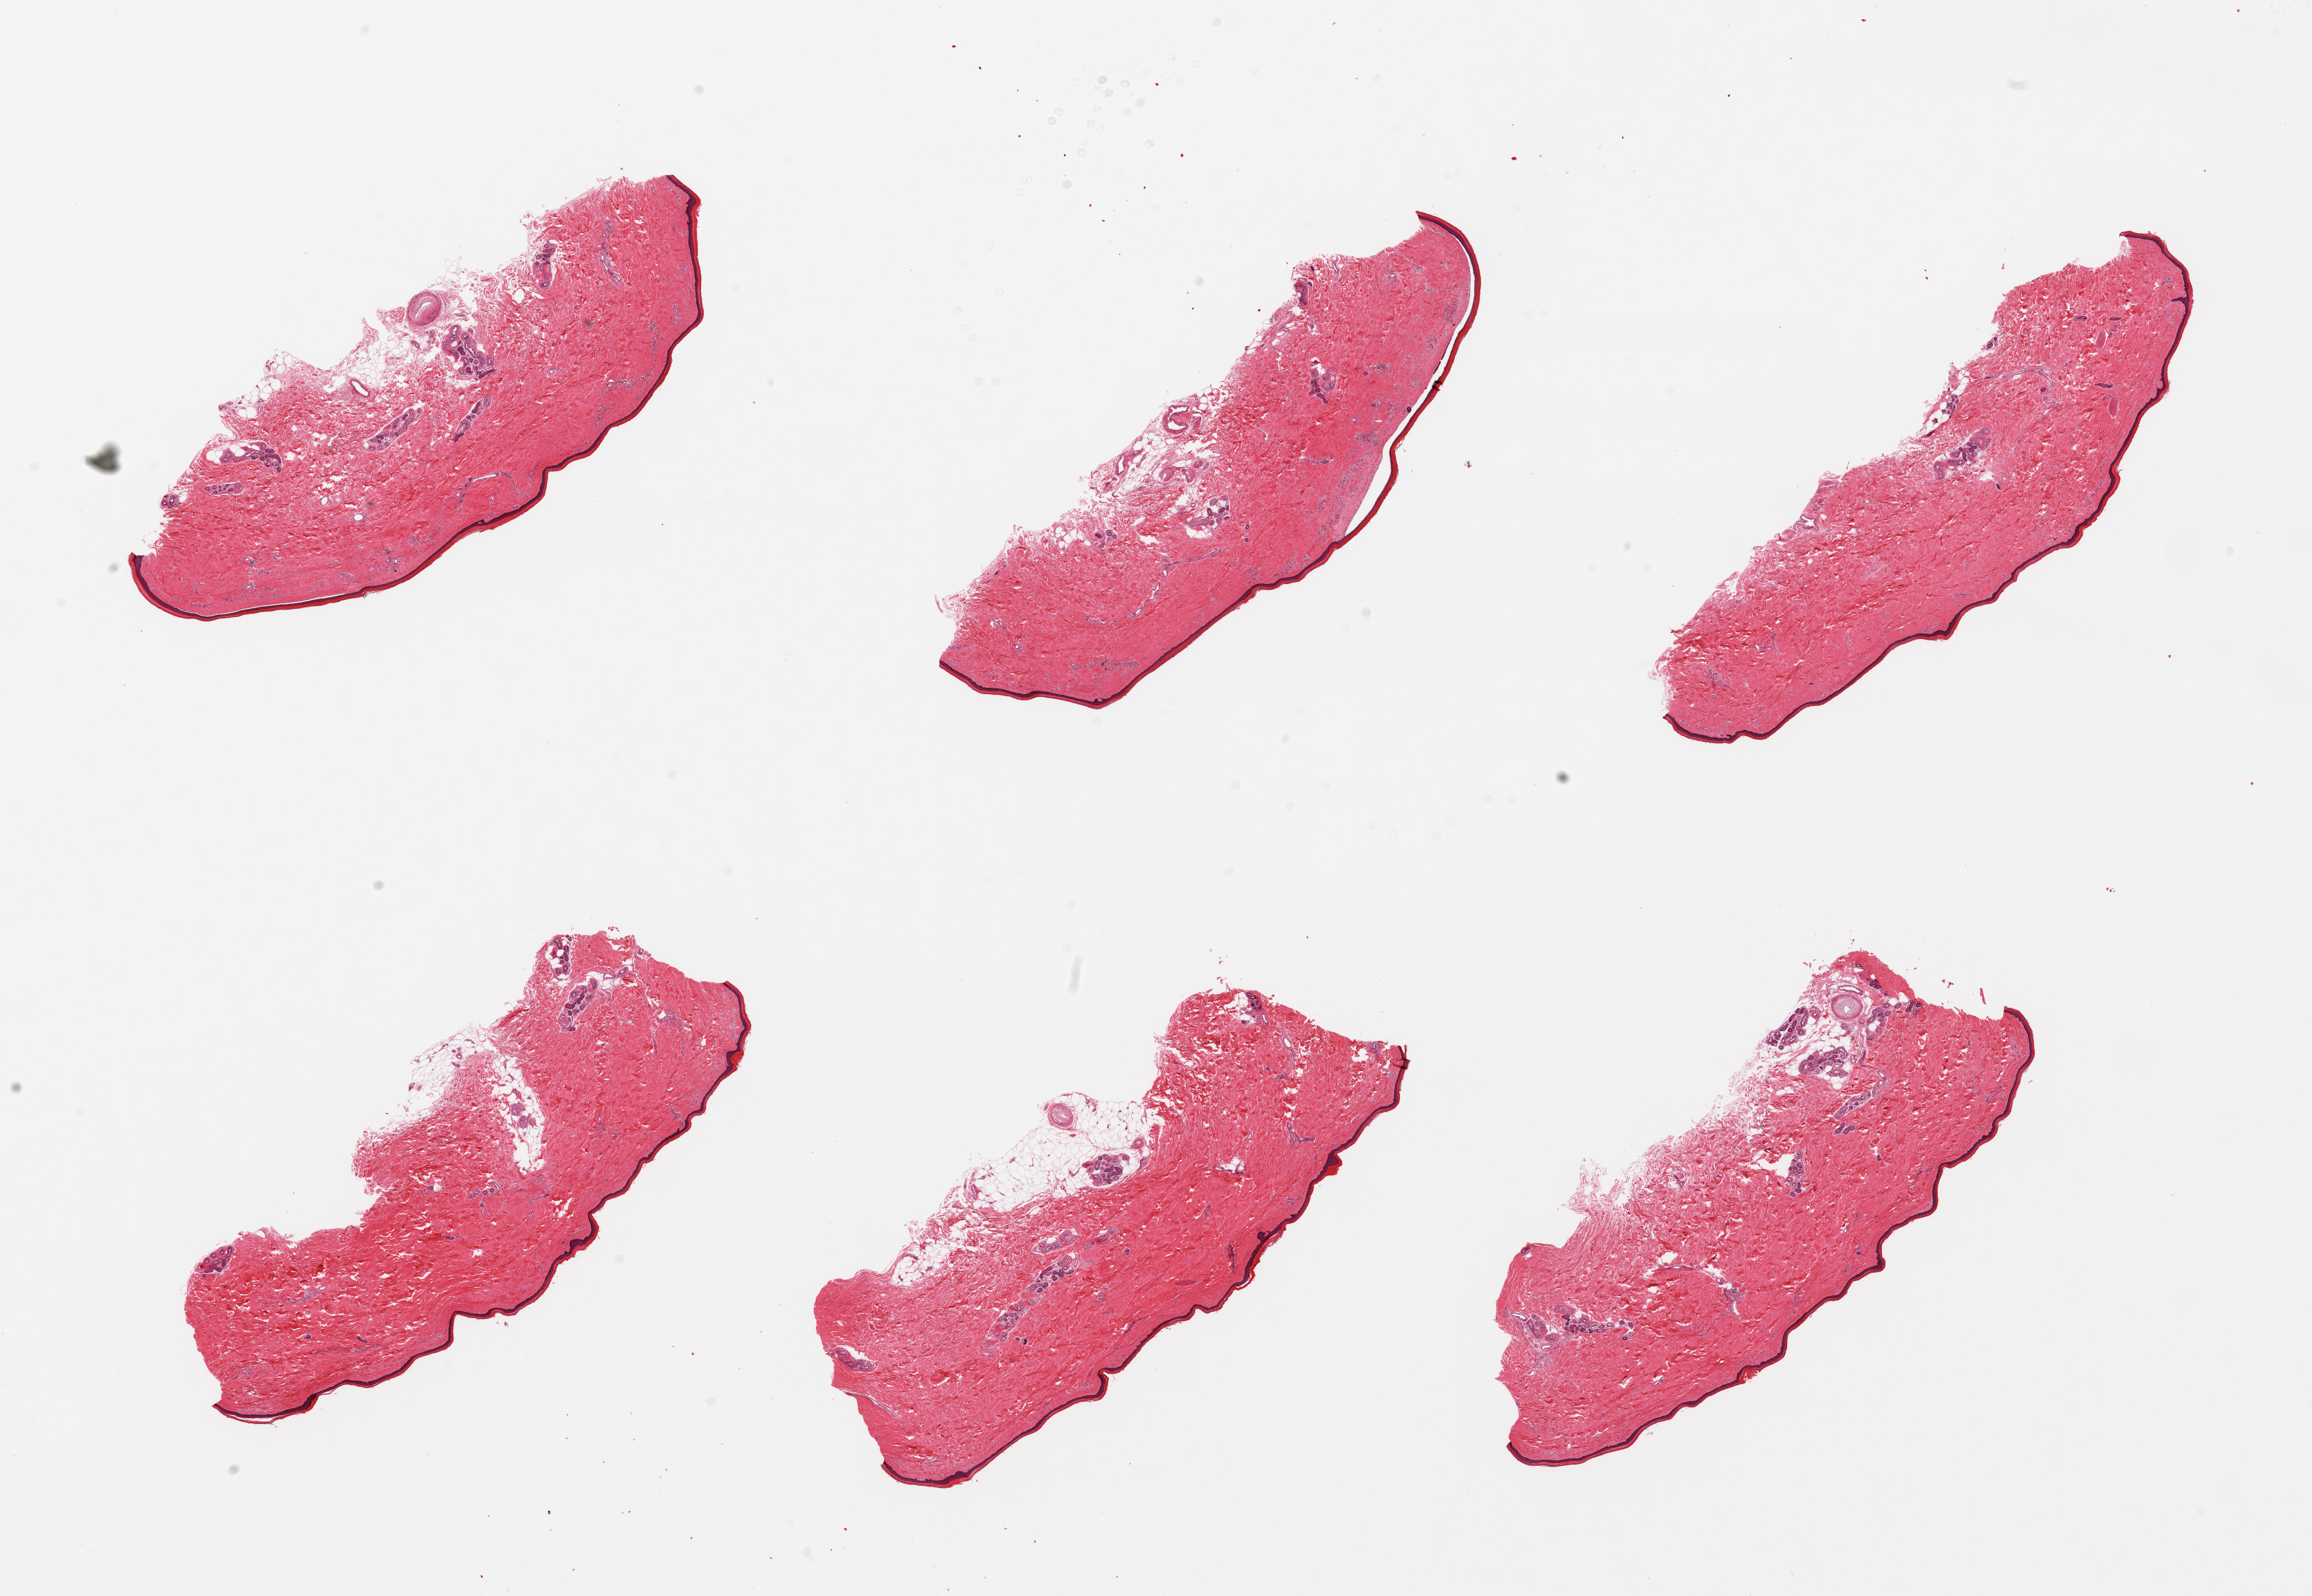
H&E whole-slide image — whole scanned area (about 26.6 x 18.3 mm) shown as a low-resolution overview. PAXgene-fixed, paraffin-embedded tissue. Sampled site (target tissue): skin of lower leg. Donor tissue sample. Donor: male.
Reviewer comment on this tissue sample: 6 pieces; well dissected.